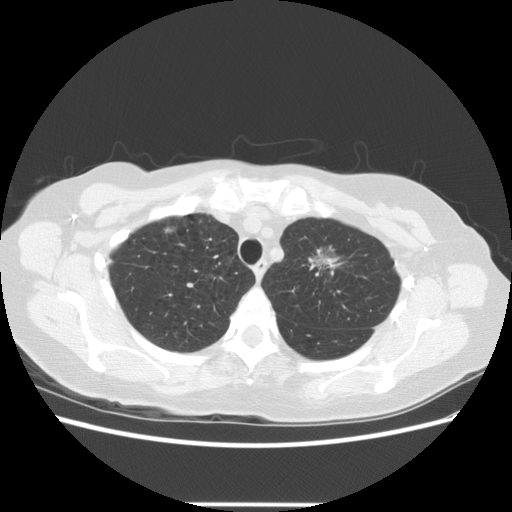
Low-dose screening chest CT, one axial slice; position 101 of 126 along the scan axis; reconstruction kernel STANDARD; lung window (W 1500 / L -600 HU); 2.5 mm slice thickness; 512 × 512 image matrix, field of view 360 × 360 mm.
Annotated regions visible in this slice (outlined manually by an expert reader):
- lesion 2 (tumor, upper lobe of left lung): box from (x=314, y=252) to (x=336, y=271) px